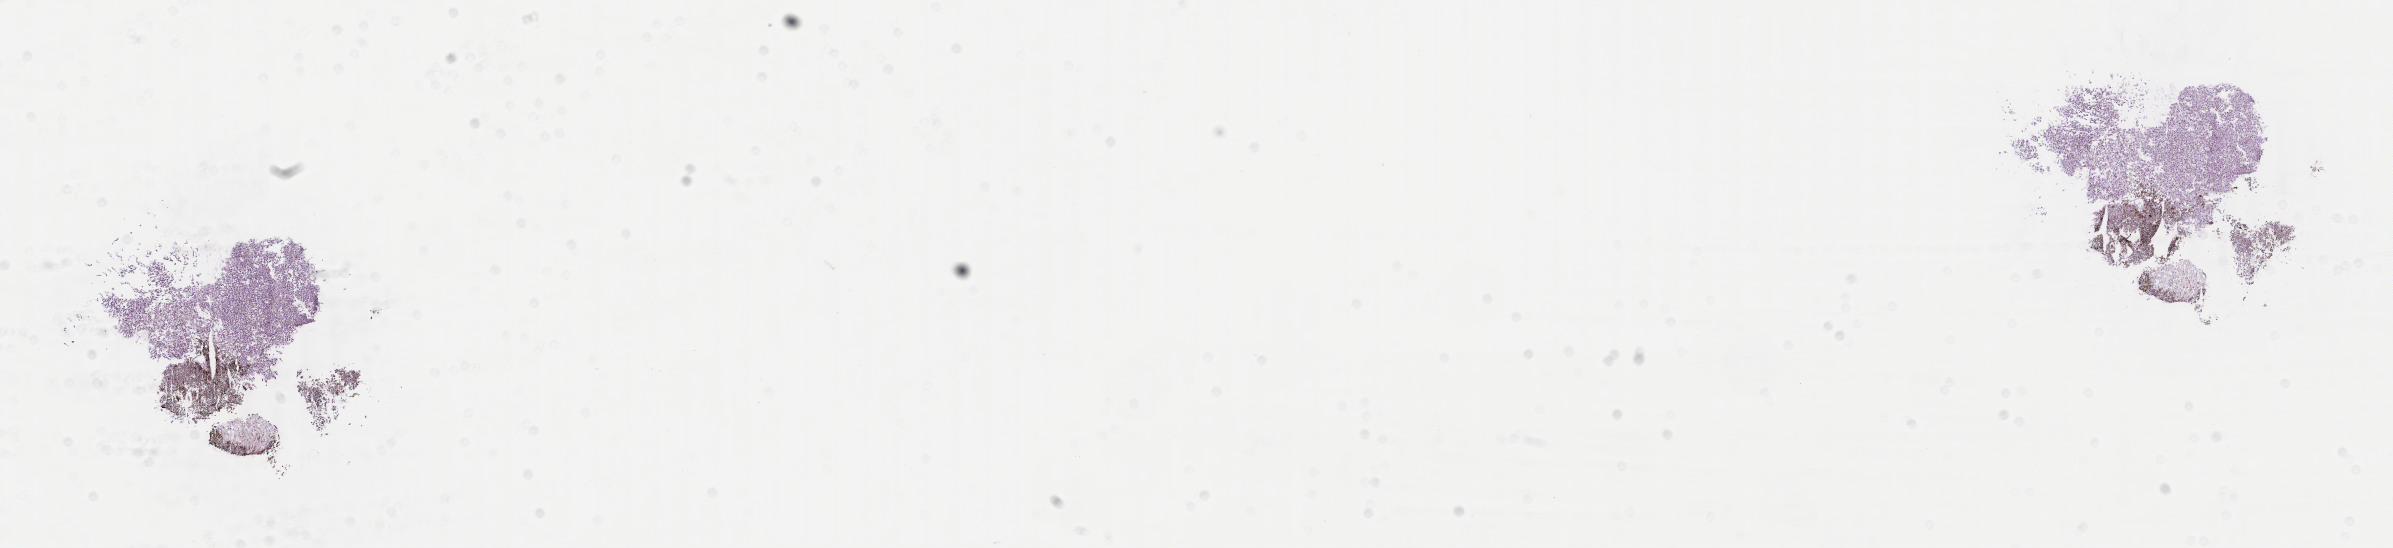
Hematoxylin and eosin (H&E) stained whole-slide image, shown as a low-resolution overview of the whole scanned area (about 19.0 x 4.4 mm). Frozen section from the top of the tissue portion. Primary tumour sample from the uvea. Male, age 68 years at initial diagnosis. Composition of this section per pathologist review: tumour cells 95%, tumour nuclei 95%, normal cells 0%, stromal cells 5%, necrosis 0%. Infiltration values recorded for this section: lymphocyte infiltration 0%, monocyte infiltration 0%, neutrophil infiltration 0%.
Diagnosis: Mixed epithelioid and spindle cell melanoma (choroid). AJCC pathologic stage: IIIA (7th edition).